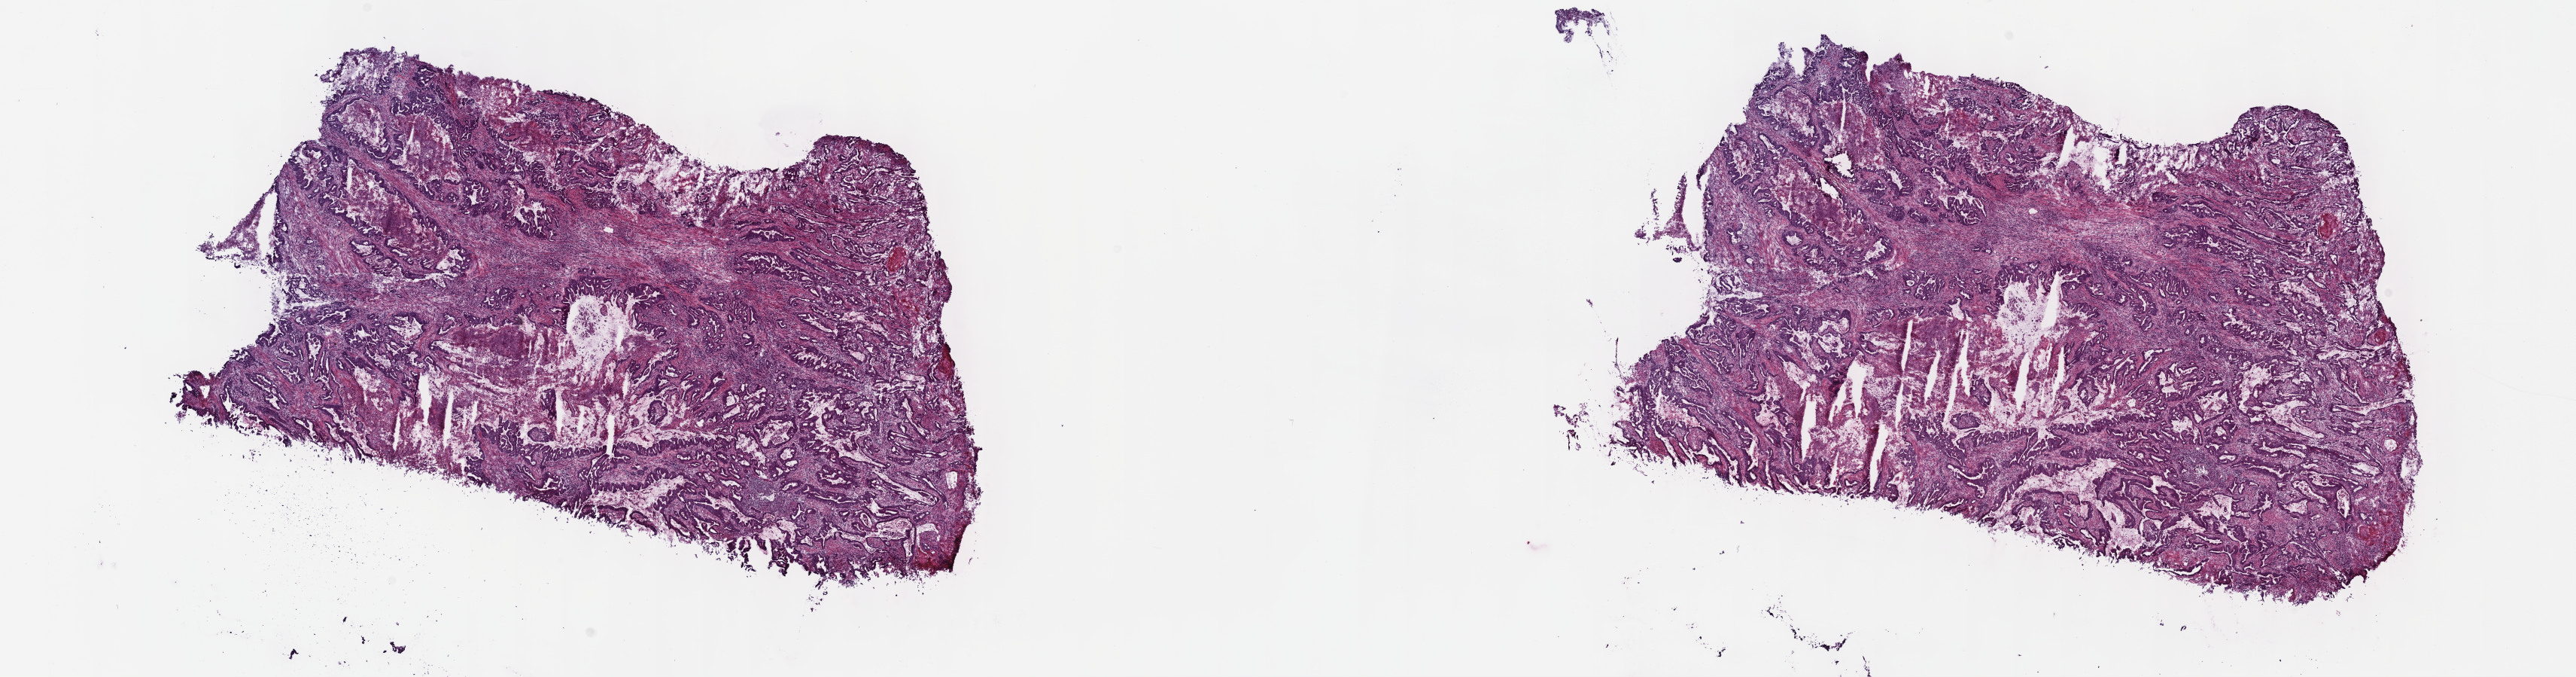
Digitized H&E tissue section (whole slide), a low-resolution overview of the entire scanned area, about 27.7 x 7.3 mm. Frozen section from the top of the tissue portion. Primary tumour sample from the stomach. Patient: female, age at initial diagnosis 65 years. Histologic grade: G2 (moderately differentiated). Composition of this section per pathologist review: tumour cells 50%, tumour nuclei 60%, normal cells 10%, stromal cells 40%, necrosis 0%. Infiltration values recorded for this section: lymphocyte infiltration 0%, monocyte infiltration 0%, neutrophil infiltration 0%.
Lymph nodes positive (case pathology): 0 of 47 examined. AJCC pathologic stage: II (6th edition). TNM: T3 N0 M0. Diagnosis: Papillary adenocarcinoma, NOS (gastric antrum).